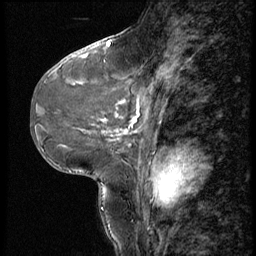
Breast MRI (dynamic contrast-enhanced), one sagittal slice; slice 27 of 56 in the series (ordered by position); 3 images stored at this slice position (order not interpretable as contrast timing); 1.5 T; TE 4.2 ms, TR 9 ms; 256 × 256 image matrix, field of view 180 × 180 mm. Patient: female, 46 years. From the clinical record (not read from this slice): setting: breast cancer imaged before/during neoadjuvant chemotherapy; receptor status: HER2-positive.
Structures marked on this image (semi-automatic segmentation, software-assisted and operator-edited):
- analysis volume of interest (the breast-tissue region the enhancement analysis was run in; not a lesion): bounding box <79,68,188,143> (left, top, right, bottom; pixels)
- tumour enhancement mask (voxels above the 140 % enhancement threshold inside the analysis volume of interest): <116,100,139,135>